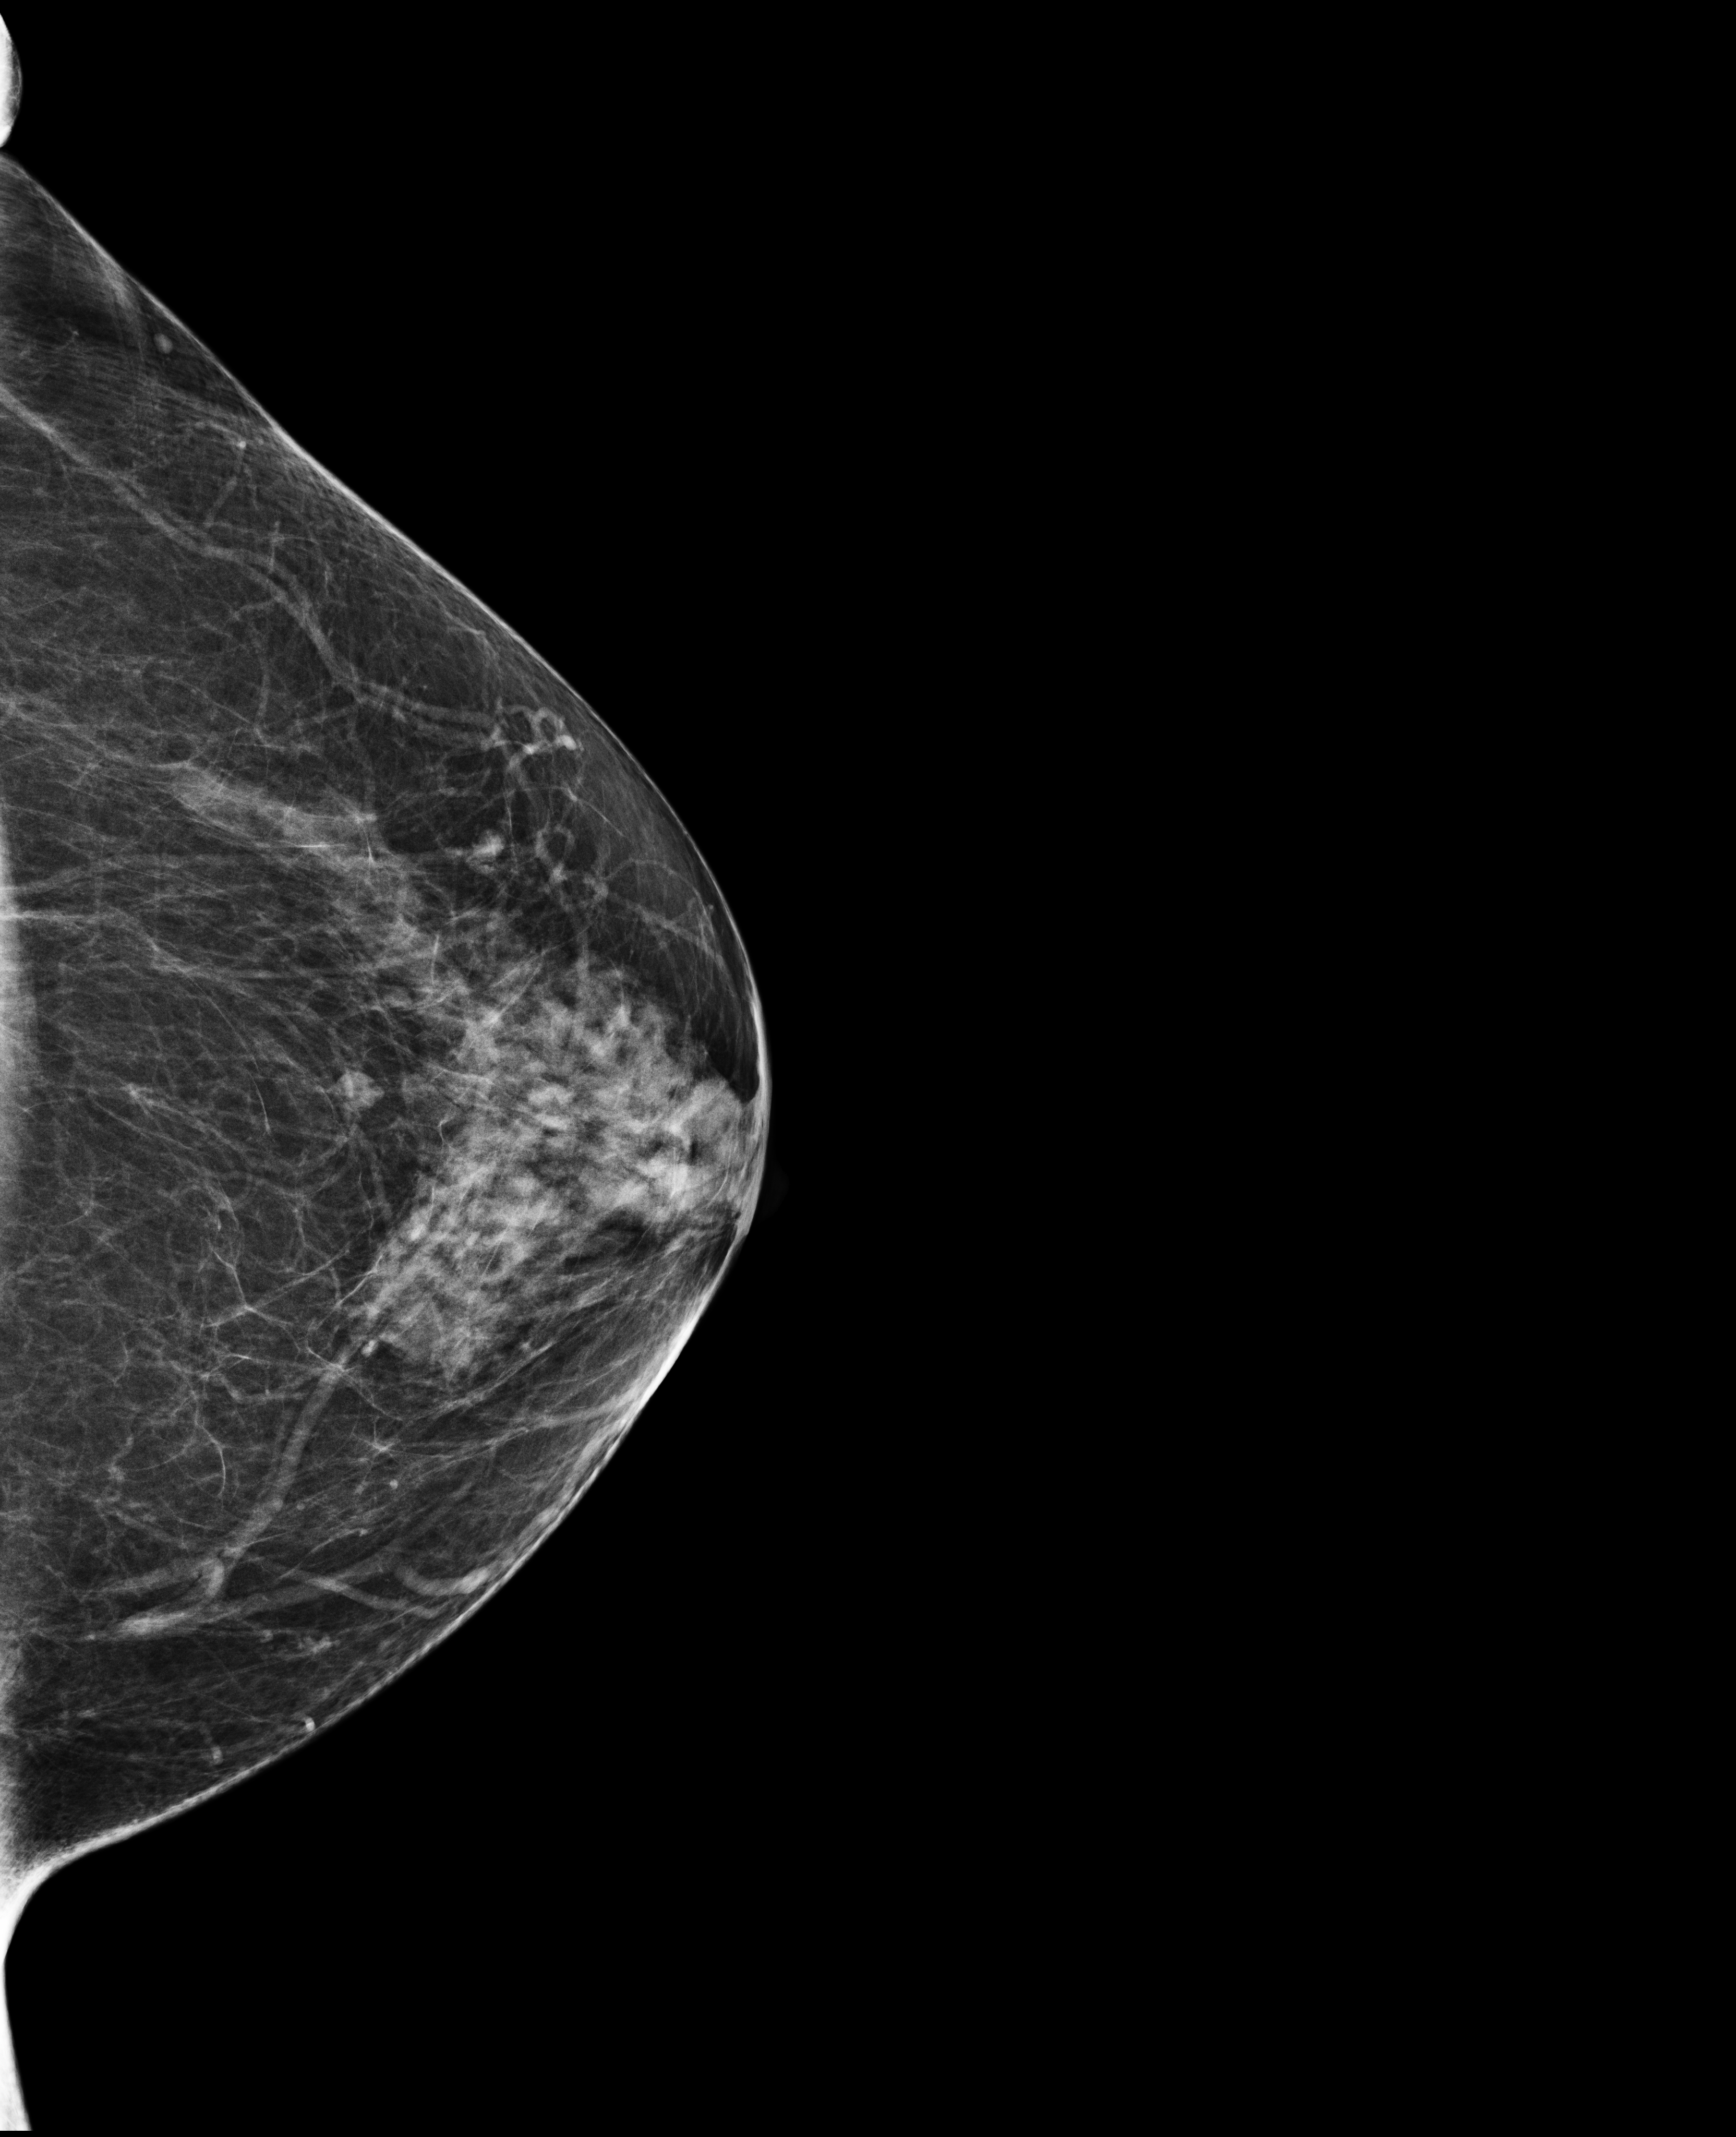
Digital mammogram (FFDM); left breast; cranio-caudal projection; screening examination. Patient aged 70 years (female).
- breast density at the screening exam (both breasts): heterogeneously dense (BI-RADS density category c)
- final BI-RADS category for the screening round (tomosynthesis exam, both breasts): category 1
- recall: no recall after this screen